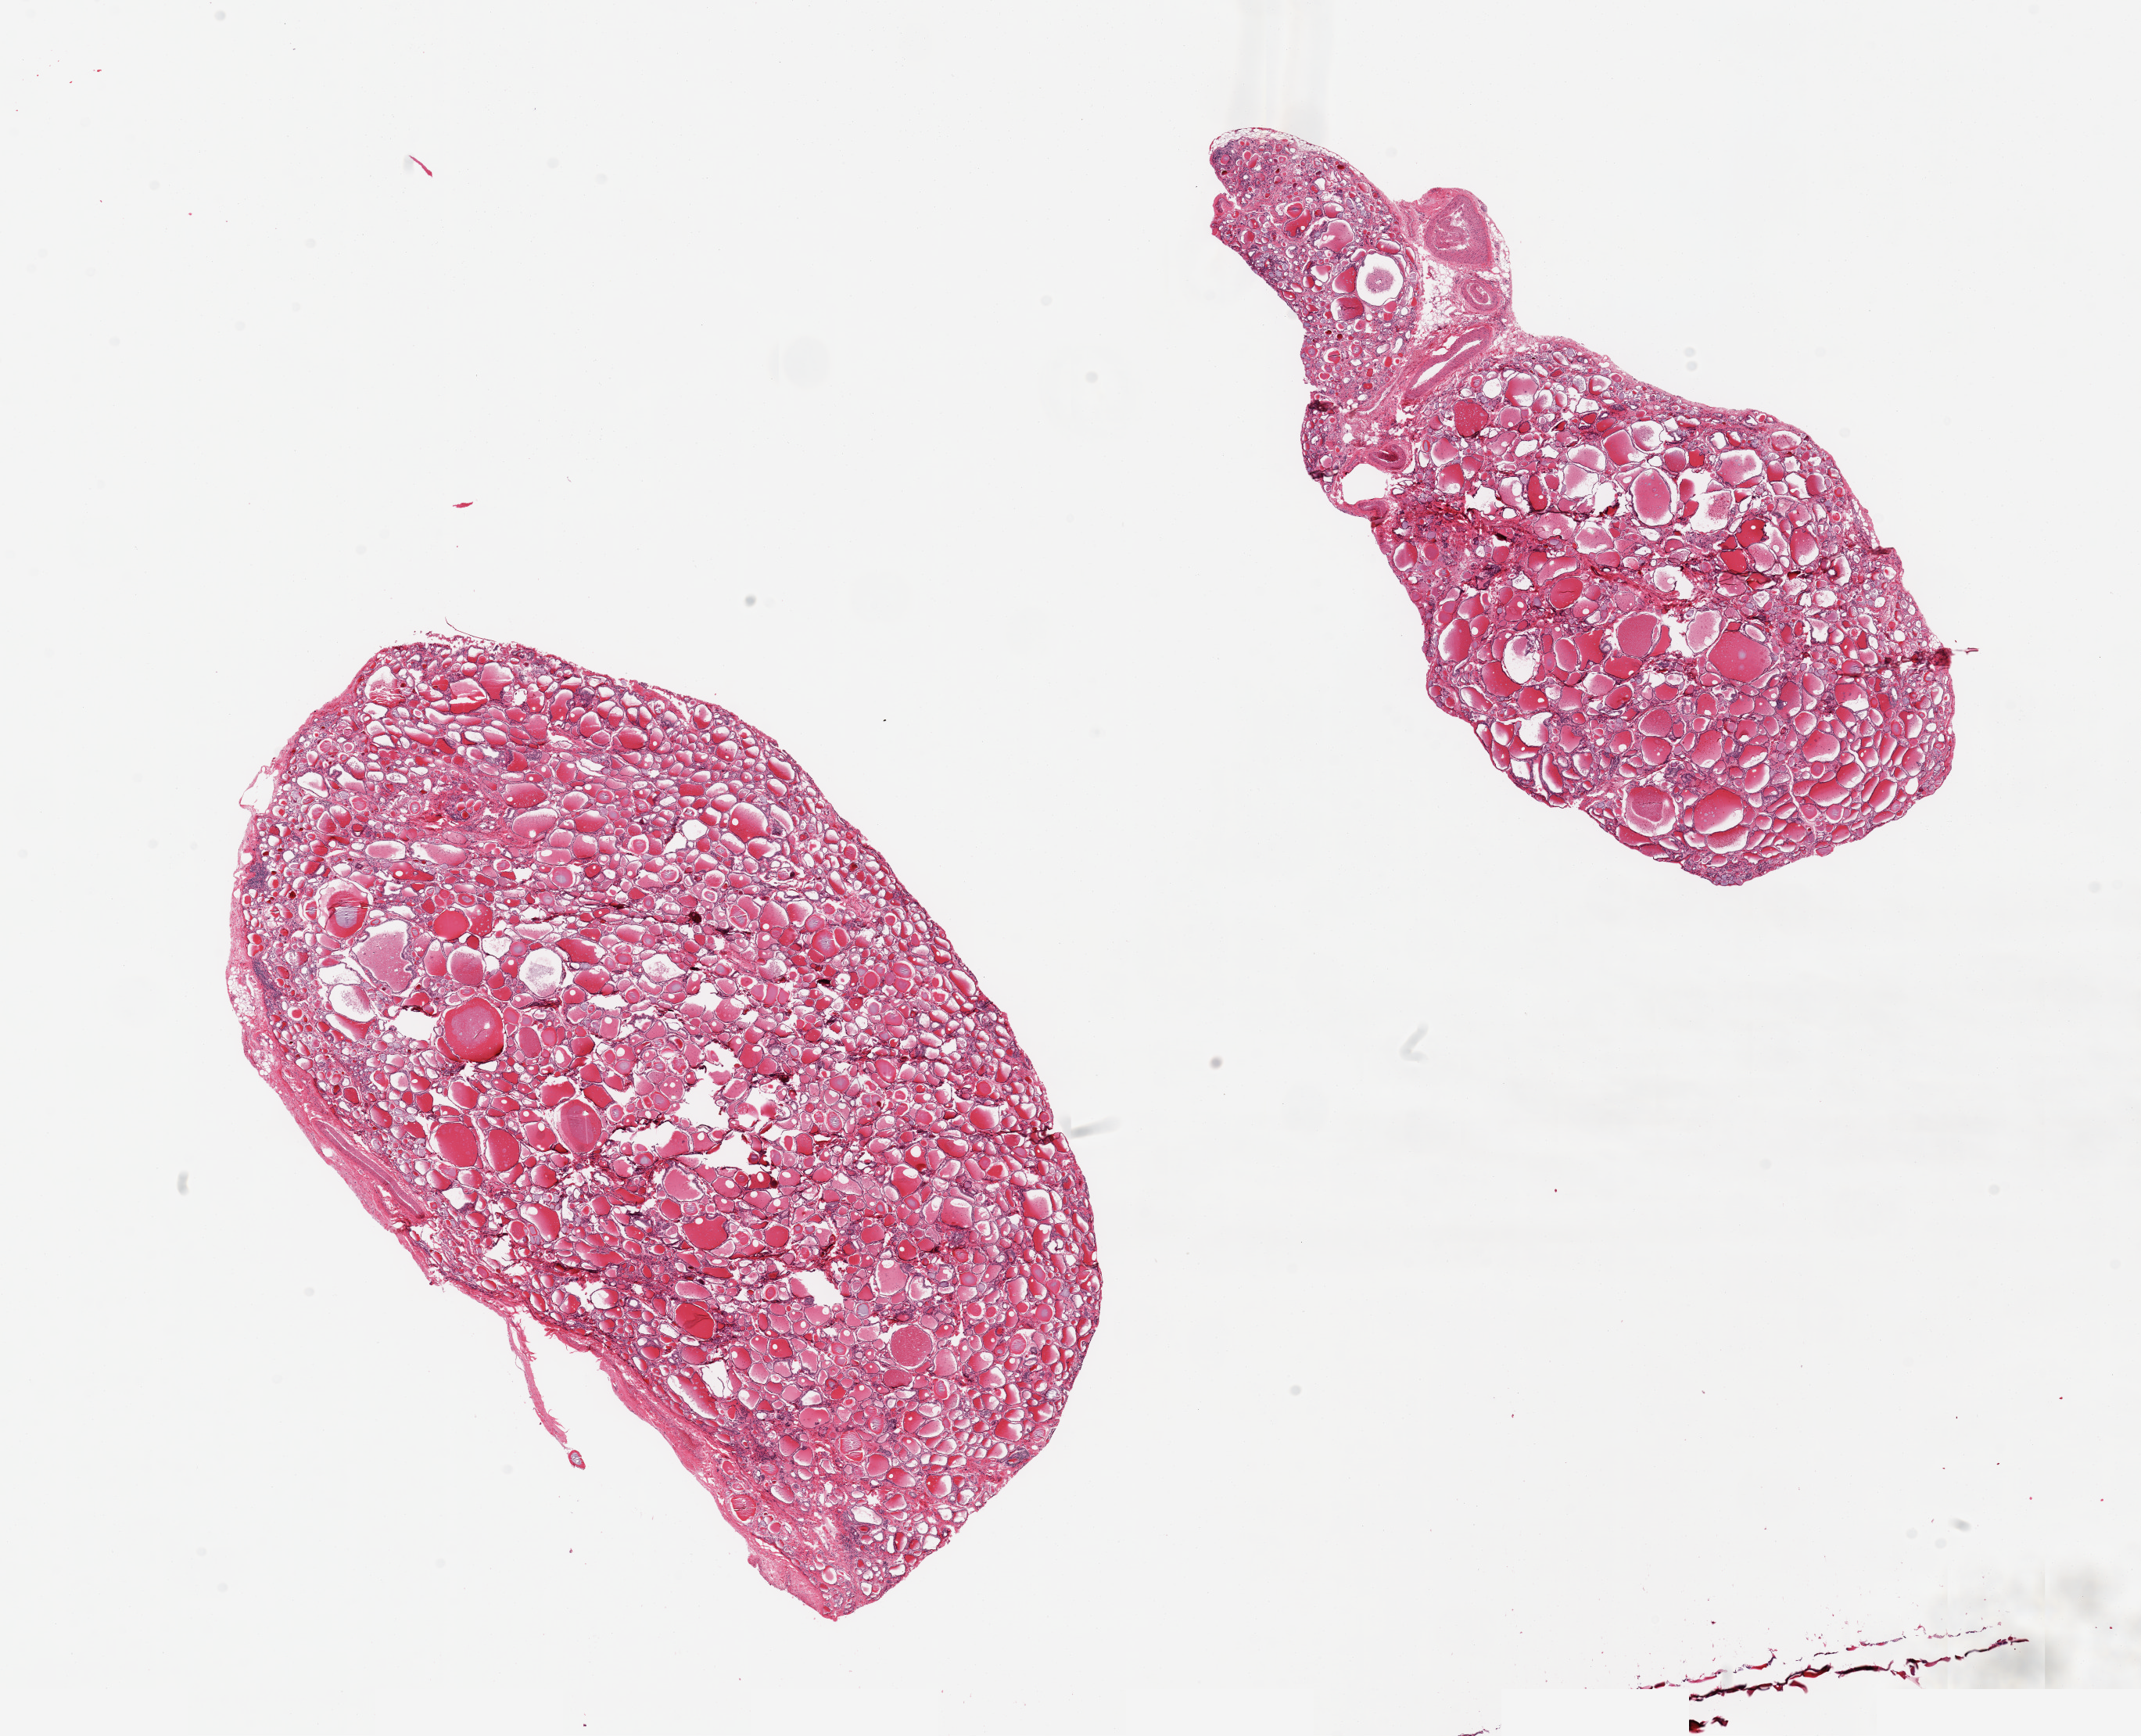
Digitized H&E-stained section, brightfield, whole scanned area (about 21.7 x 17.6 mm, slide scanned at 20x) shown as a low-resolution overview. PAXgene-fixed, paraffin-embedded tissue. Section of thyroid (target tissue). Tissue donor sample.
Reviewer comment on this tissue sample: 2 pieces; well dissected.